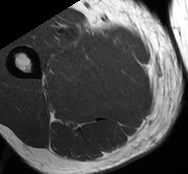
MRI of an extremity soft-tissue mass, one axial slice; position 23 of 93 along the scan axis; MR volume resampled by the dataset authors to the PET/CT grid (not the native acquisition matrix); 3.27 mm slice thickness; 188 × 174 image matrix, field of view 184 × 170 mm. Male patient. Case-level facts recorded for this patient, not image findings: histological type: undifferentiated - pleiomorphic; grade: high; site of the primary tumour: right thigh.
Outlined on this slice (expert contour drawn on MRI and transferred to this co-registered scan by the dataset authors):
- gross tumour volume including surrounding oedema: bounding box [x1, y1, x2, y2] px = [47, 31, 124, 81]